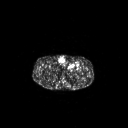
FDG PET of an extremity soft-tissue mass (from a PET/CT study), one axial slice; slice 266 of 267 in the series (ordered by position); 3.27 mm slice thickness; 128 × 128 image matrix, field of view 700 × 700 mm. Patient: male, 63 years. Case-level facts recorded for this patient, not image findings: histological type: pleiomorphic liposarcoma; grade: high; site of the primary tumour: left thigh.
Outlined on this slice (expert contour drawn on MRI and transferred to this co-registered scan by the dataset authors):
- gross tumour volume including surrounding oedema: bounding box (x1, y1, x2, y2) in pixels: (68, 62, 80, 69)
- gross tumour volume (mass): (68, 63, 76, 69)